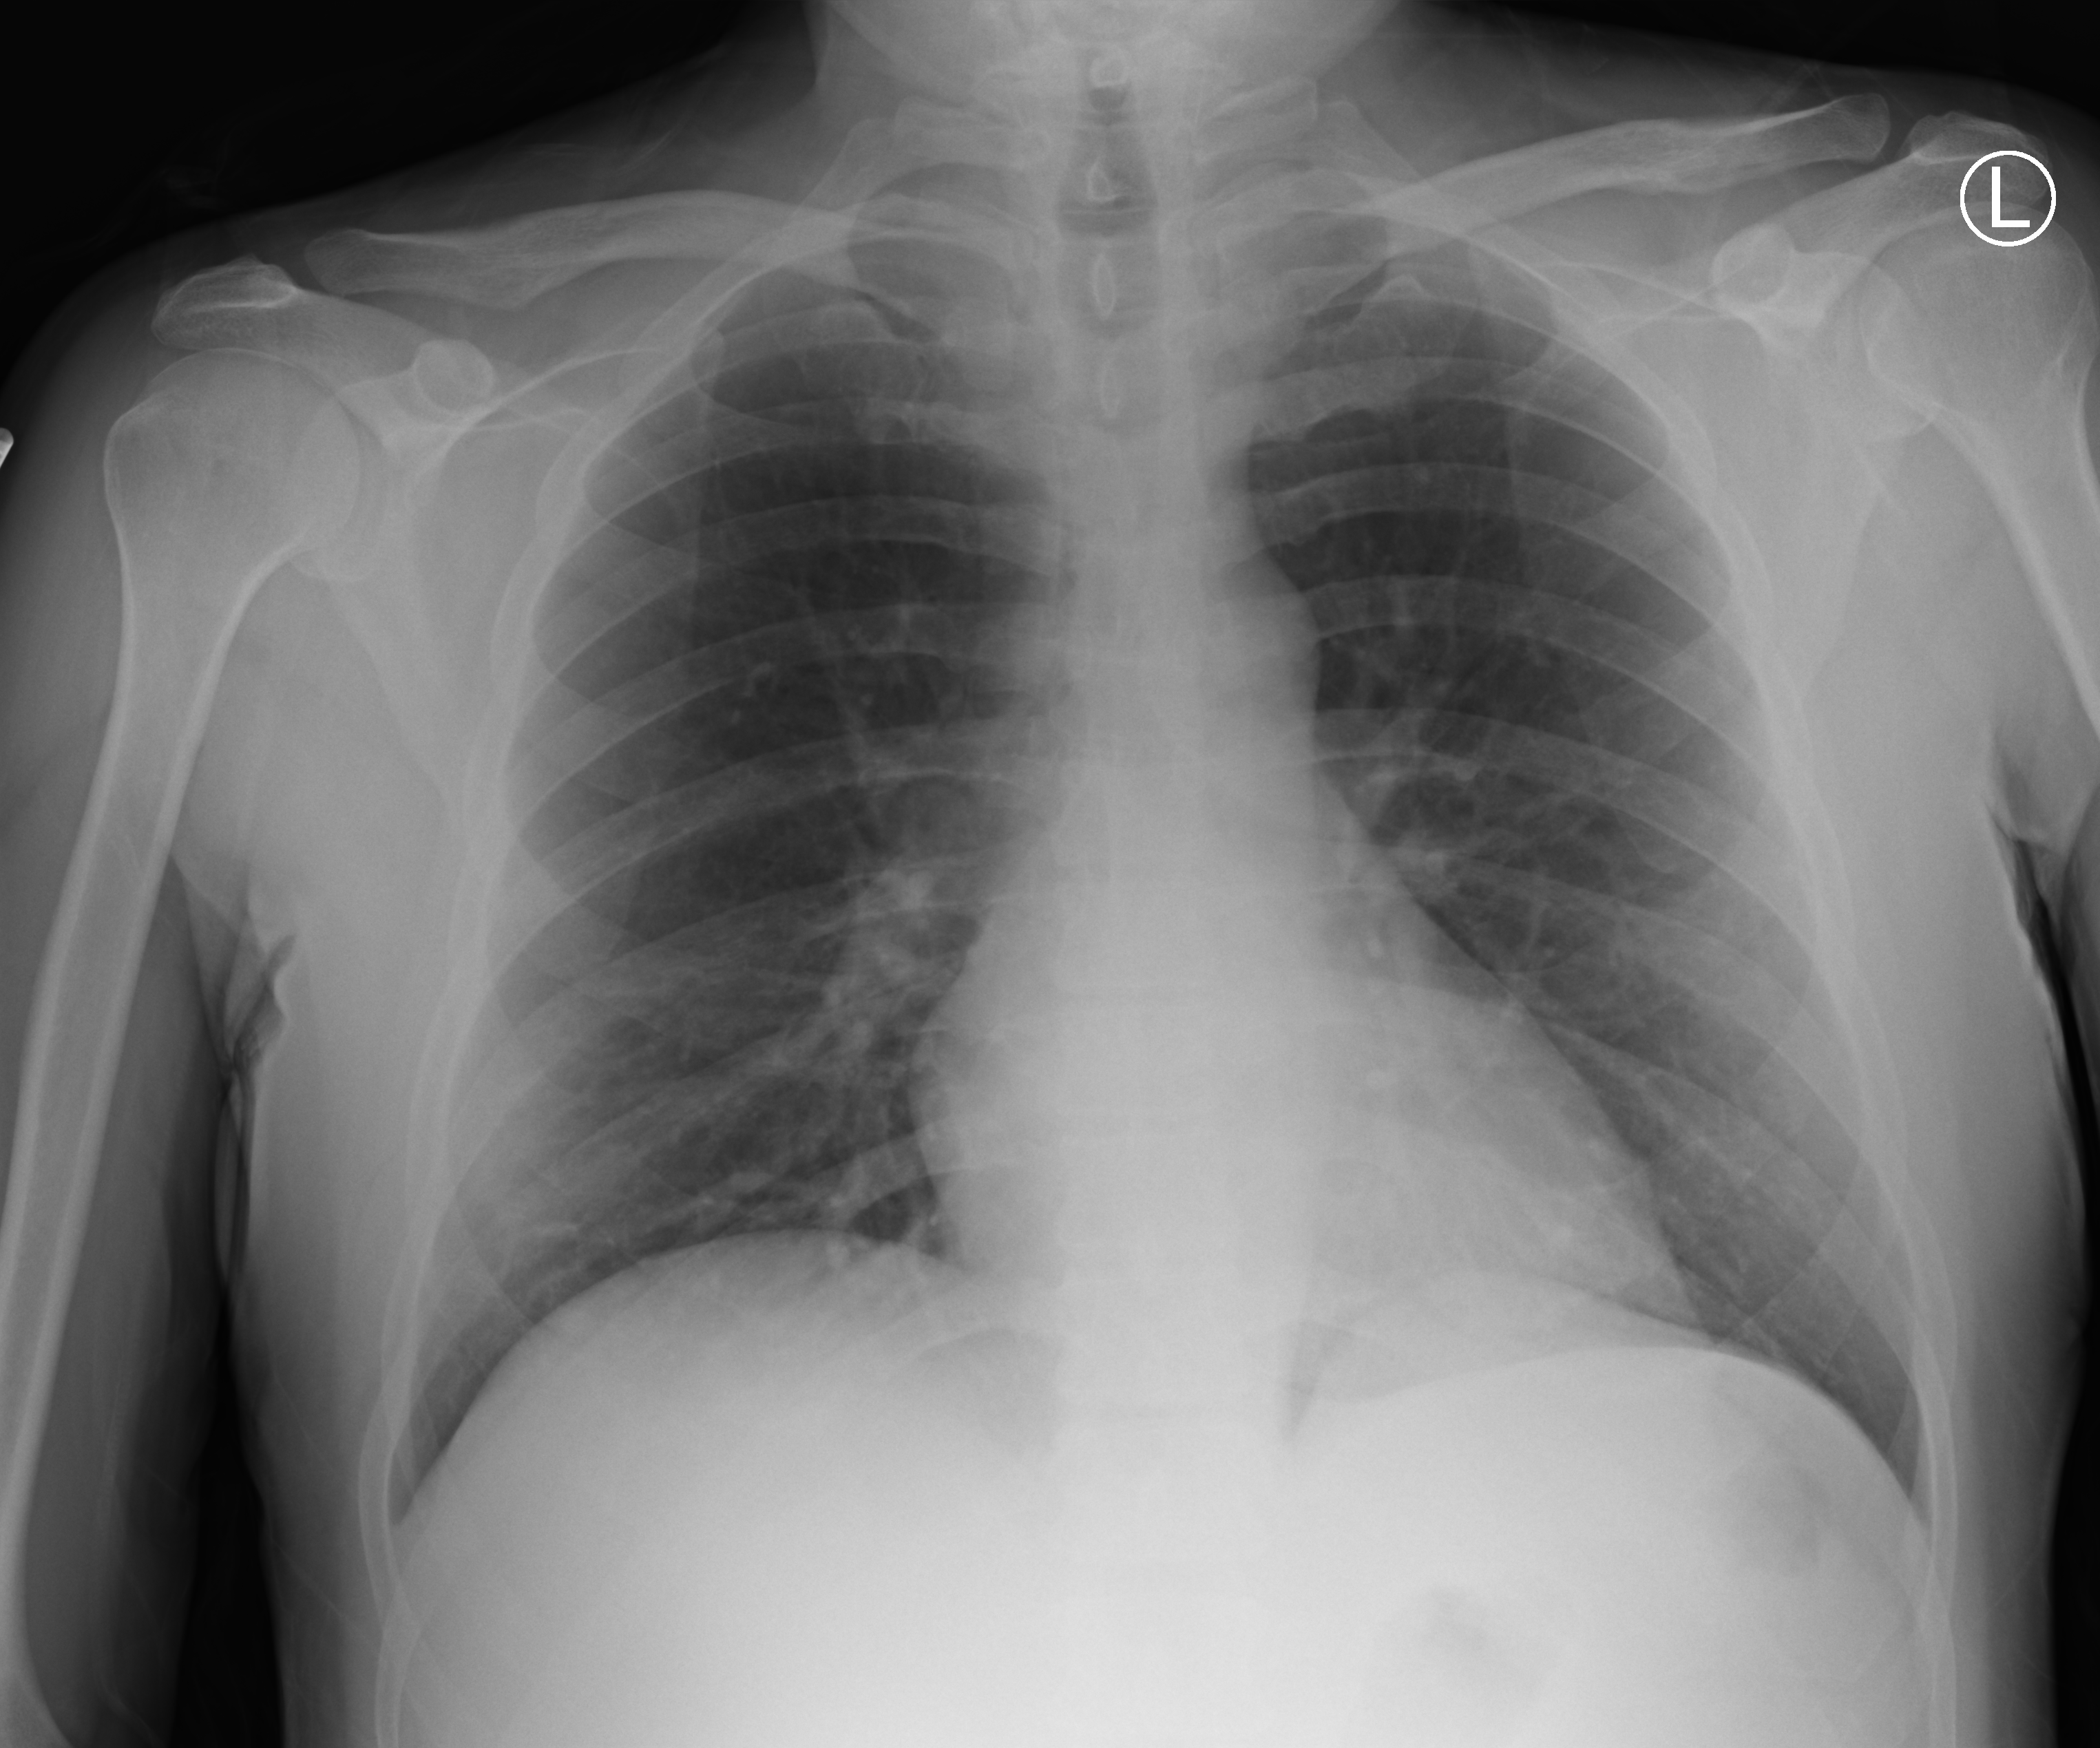
Chest X-ray (portable). Patient hospitalised with COVID-19; male, aged 18–59 years.
From the hospital-stay record, not from the radiograph (when in the stay this image was taken is not recorded):
- mechanically ventilated during this hospital stay: no